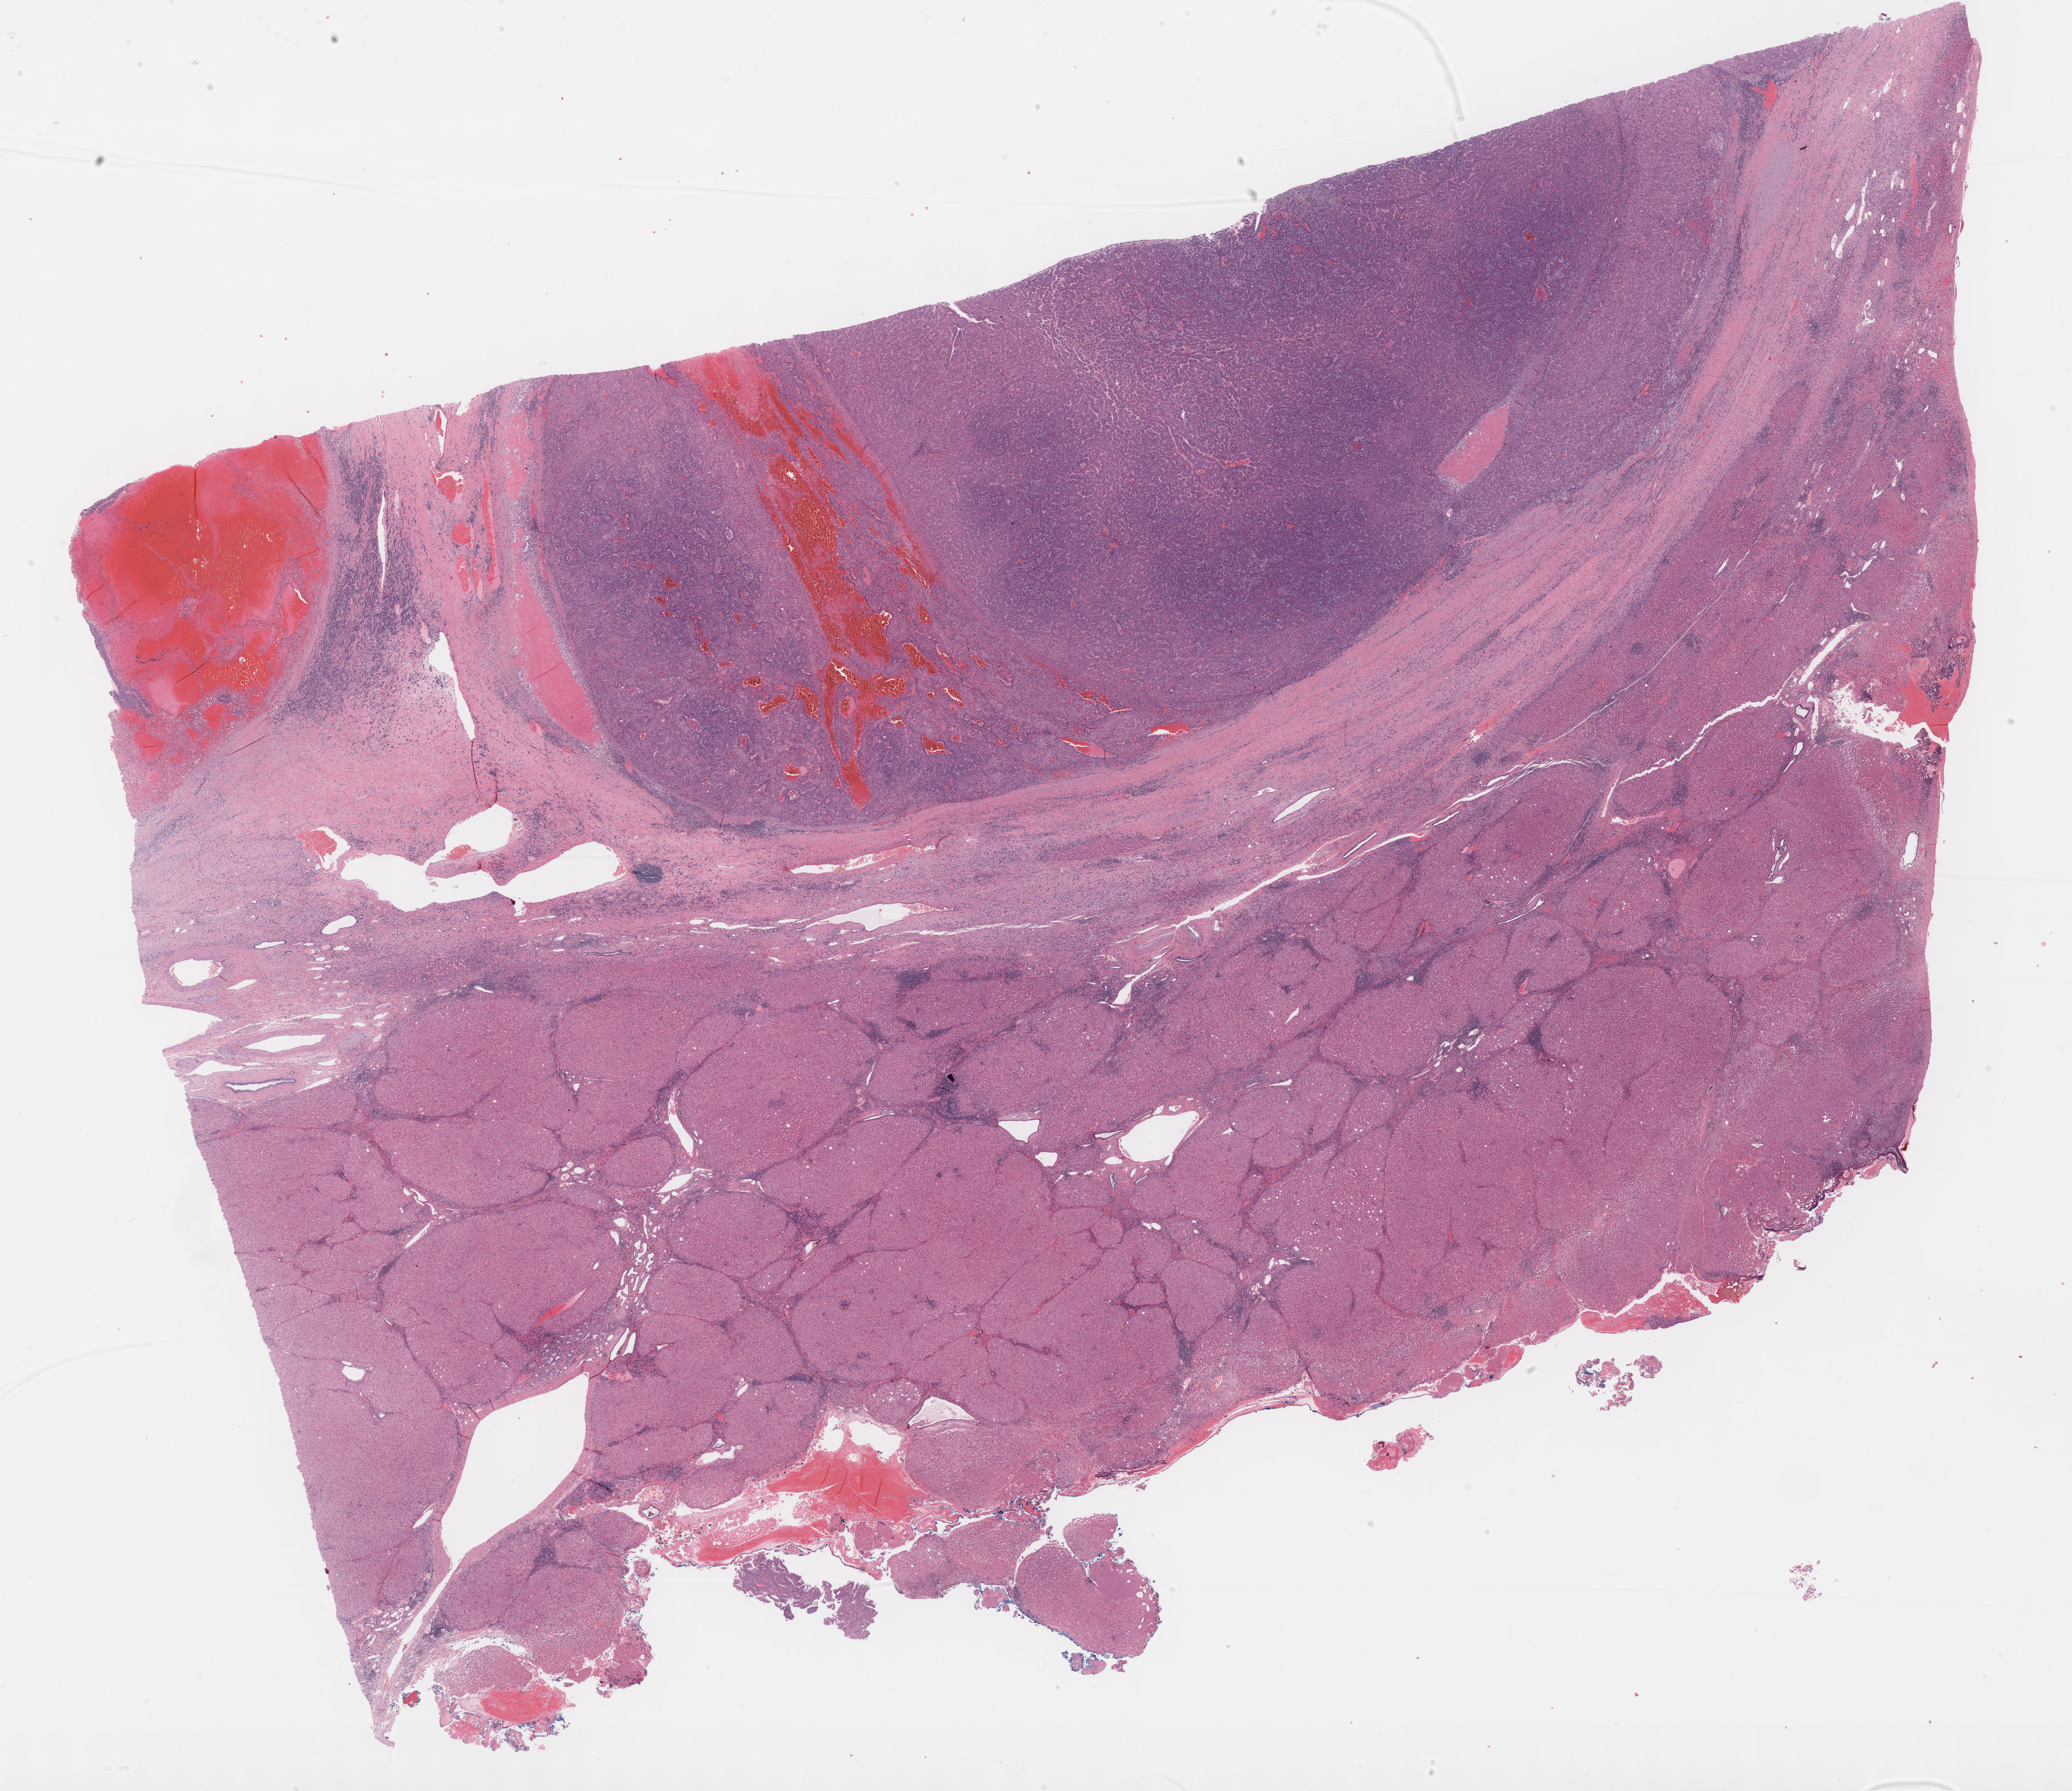
Digitized Hematoxylin and eosin (H&E) stained tissue section (whole slide) — a low-resolution overview of the entire scanned area, about 26.2 x 22.6 mm (slide scanned at 40x); formalin-fixed paraffin-embedded (FFPE) diagnostic section; liver, primary tumour sample. Female, age 58 years at initial diagnosis. Histologic grade: G2 (moderately differentiated).
- TNM: T2 N0 M0
- diagnosis: Hepatocellular carcinoma, NOS
- AJCC pathologic stage: II (7th edition)